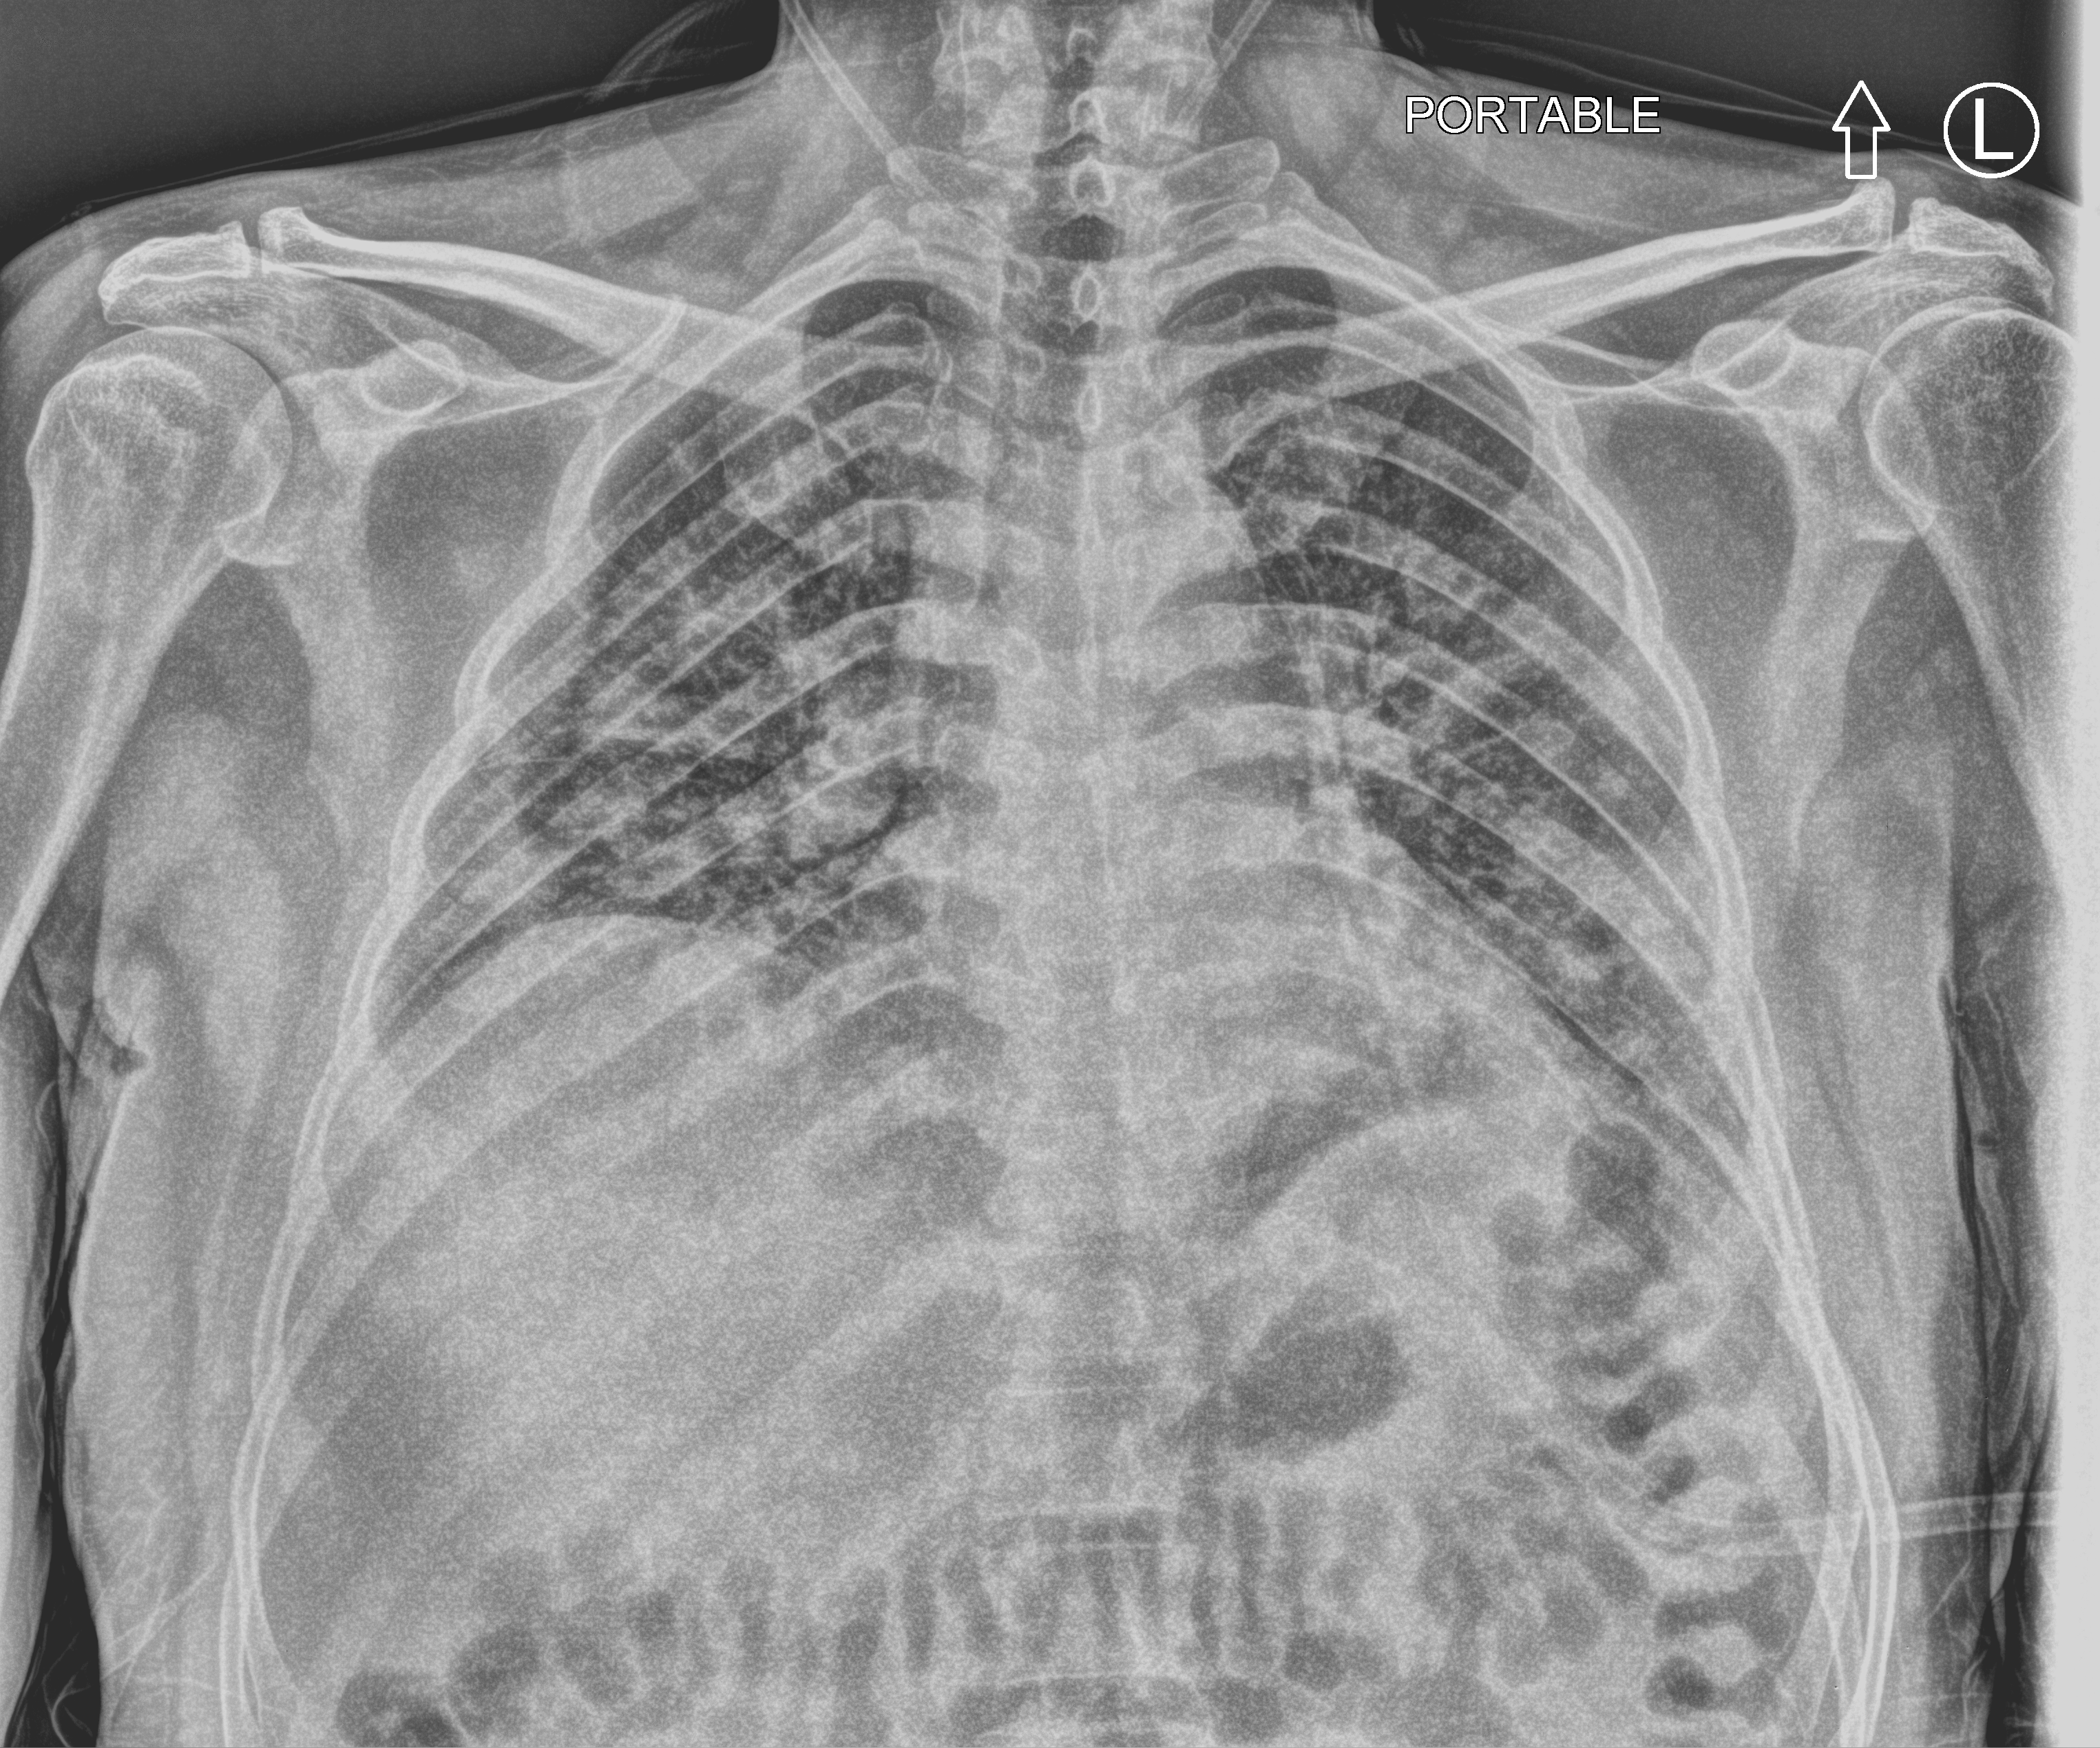
Portable chest radiograph, anteroposterior (AP) projection. Male patient hospitalised with COVID-19, age 18–59 years.
Hospital-stay facts (about this admission, not read from this image; timing relative to this image not recorded): admitted to intensive care during this hospital stay: no; other chronic lung disease (admission record): no; hypertension (admission record): no.